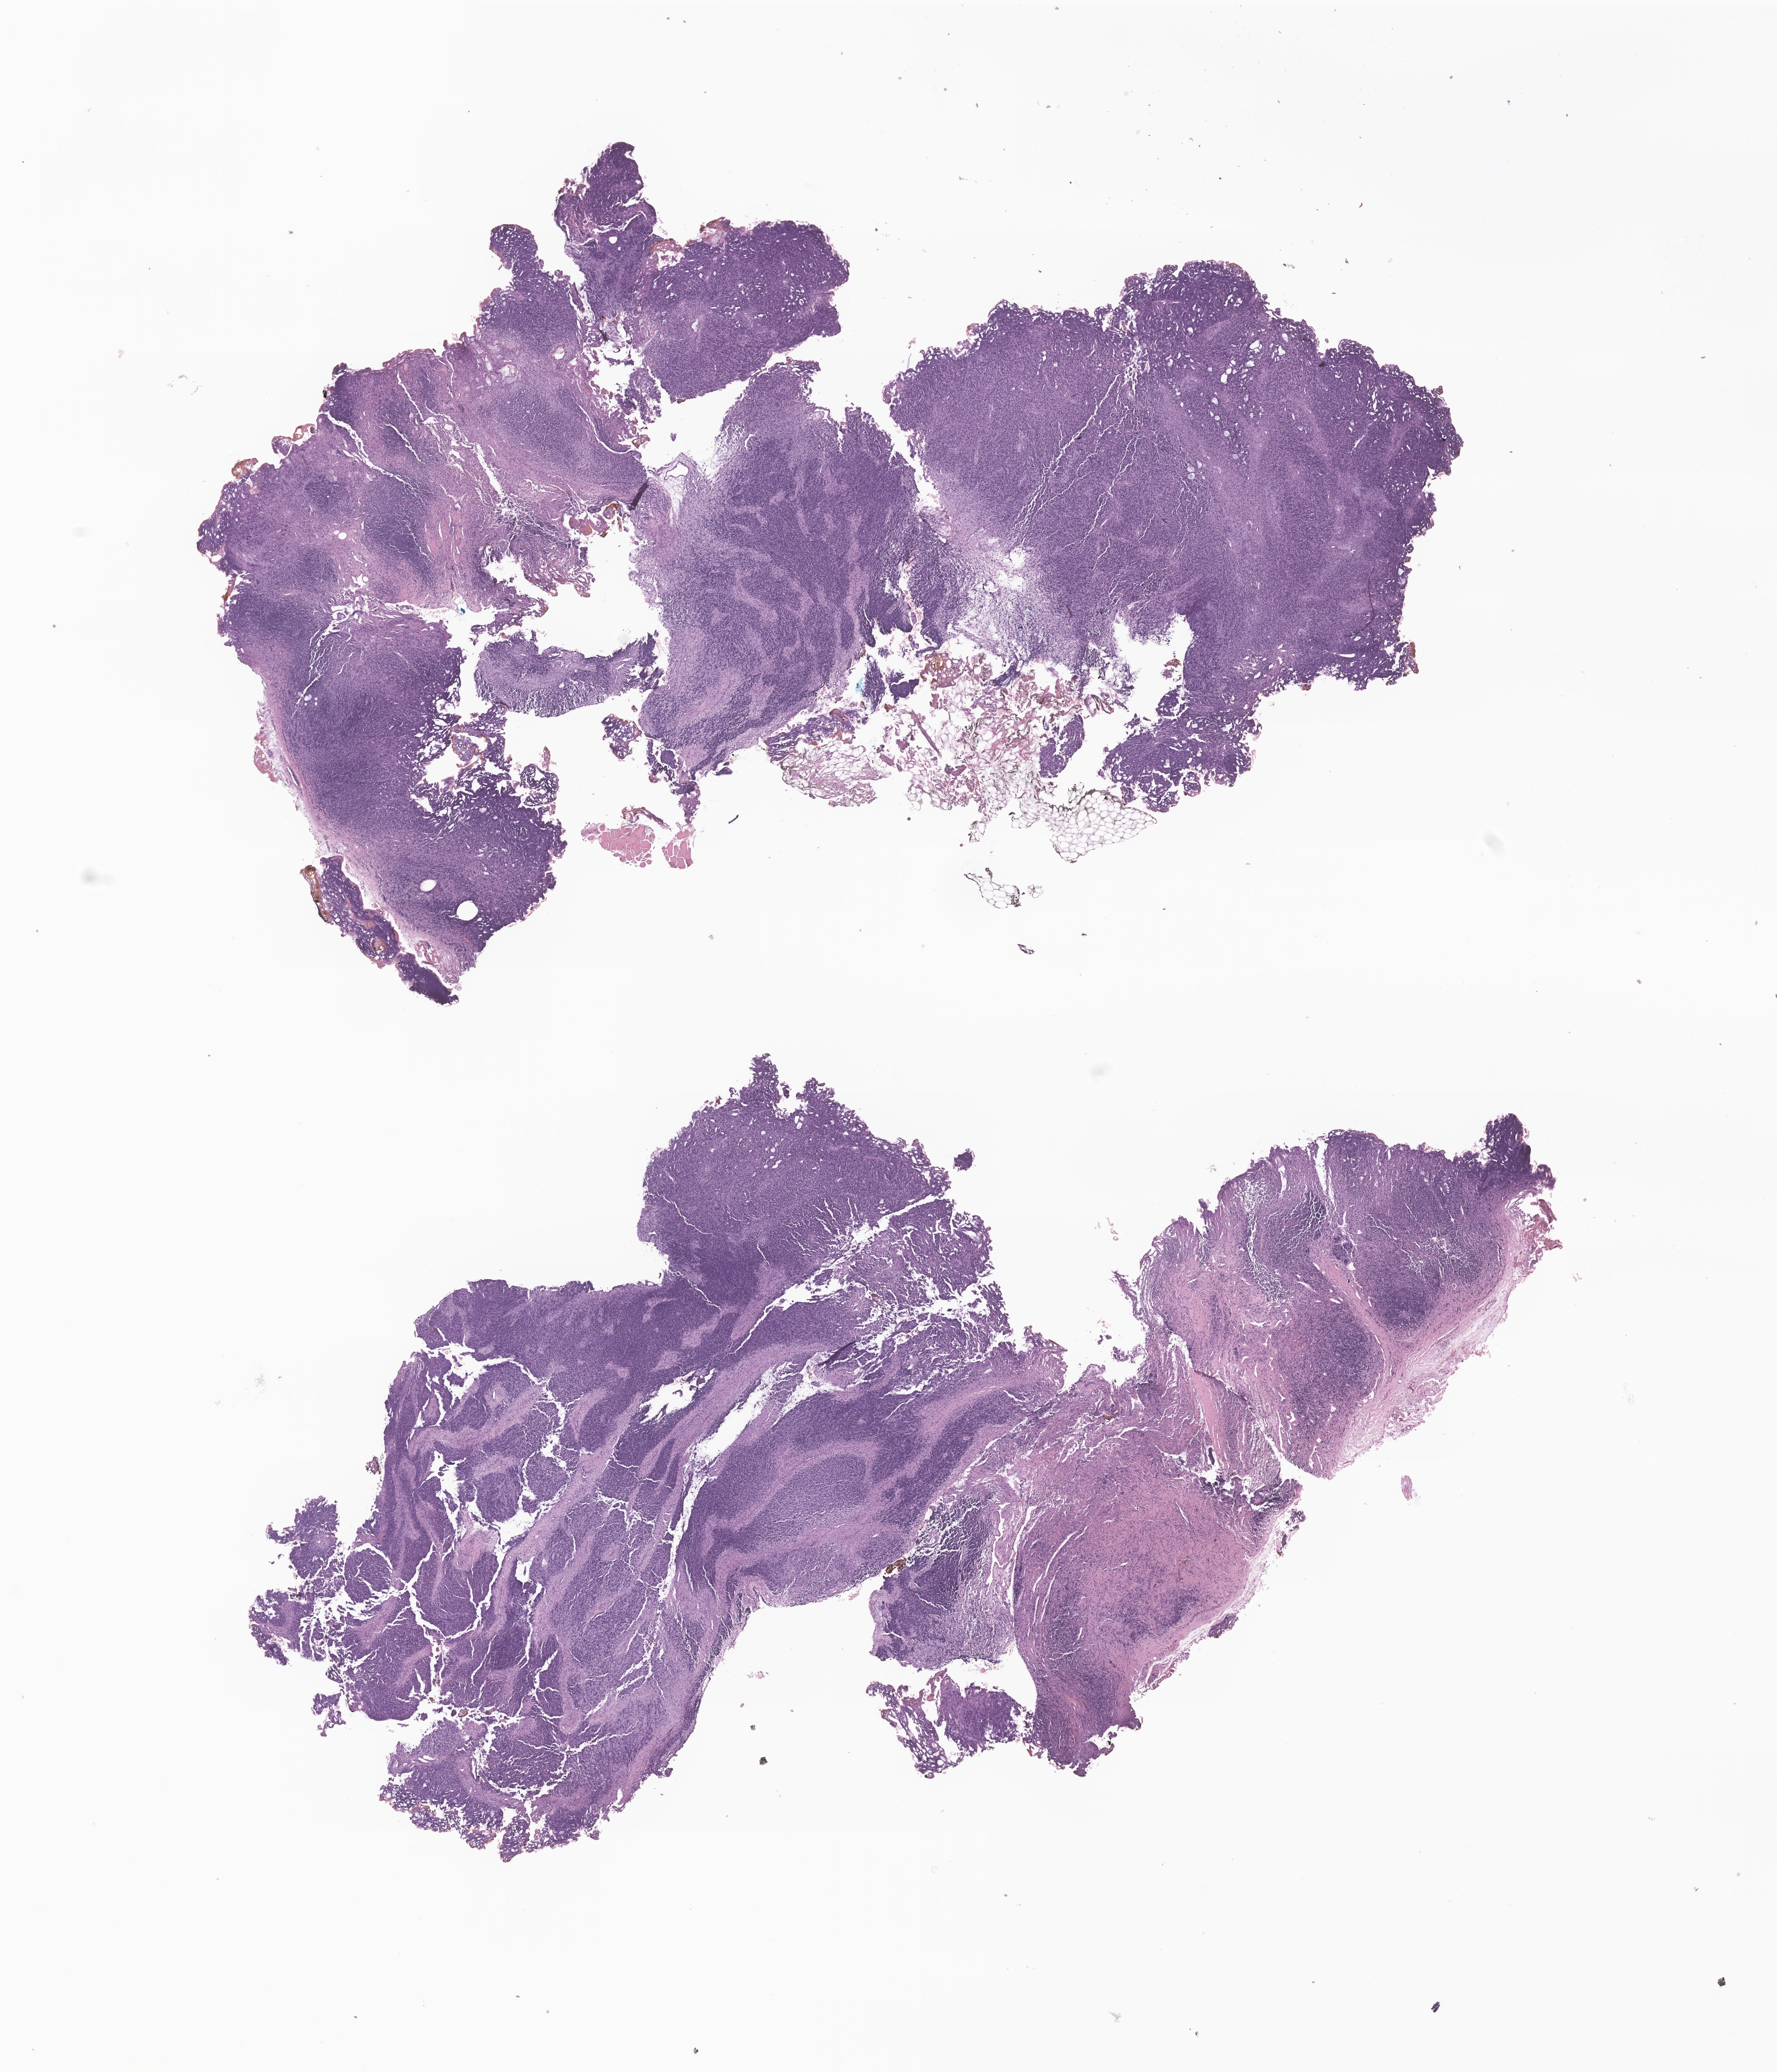
Digitized H&E-stained section of tumor tissue from the head and neck lymph node — whole scanned area (about 15.4 x 18.0 mm) shown as a low-resolution overview, formalin-fixed paraffin-embedded section. Patient: female, age 39 months (3 years 3 months).
Diagnosis: Embryonal rhabdomyosarcoma, NOS.